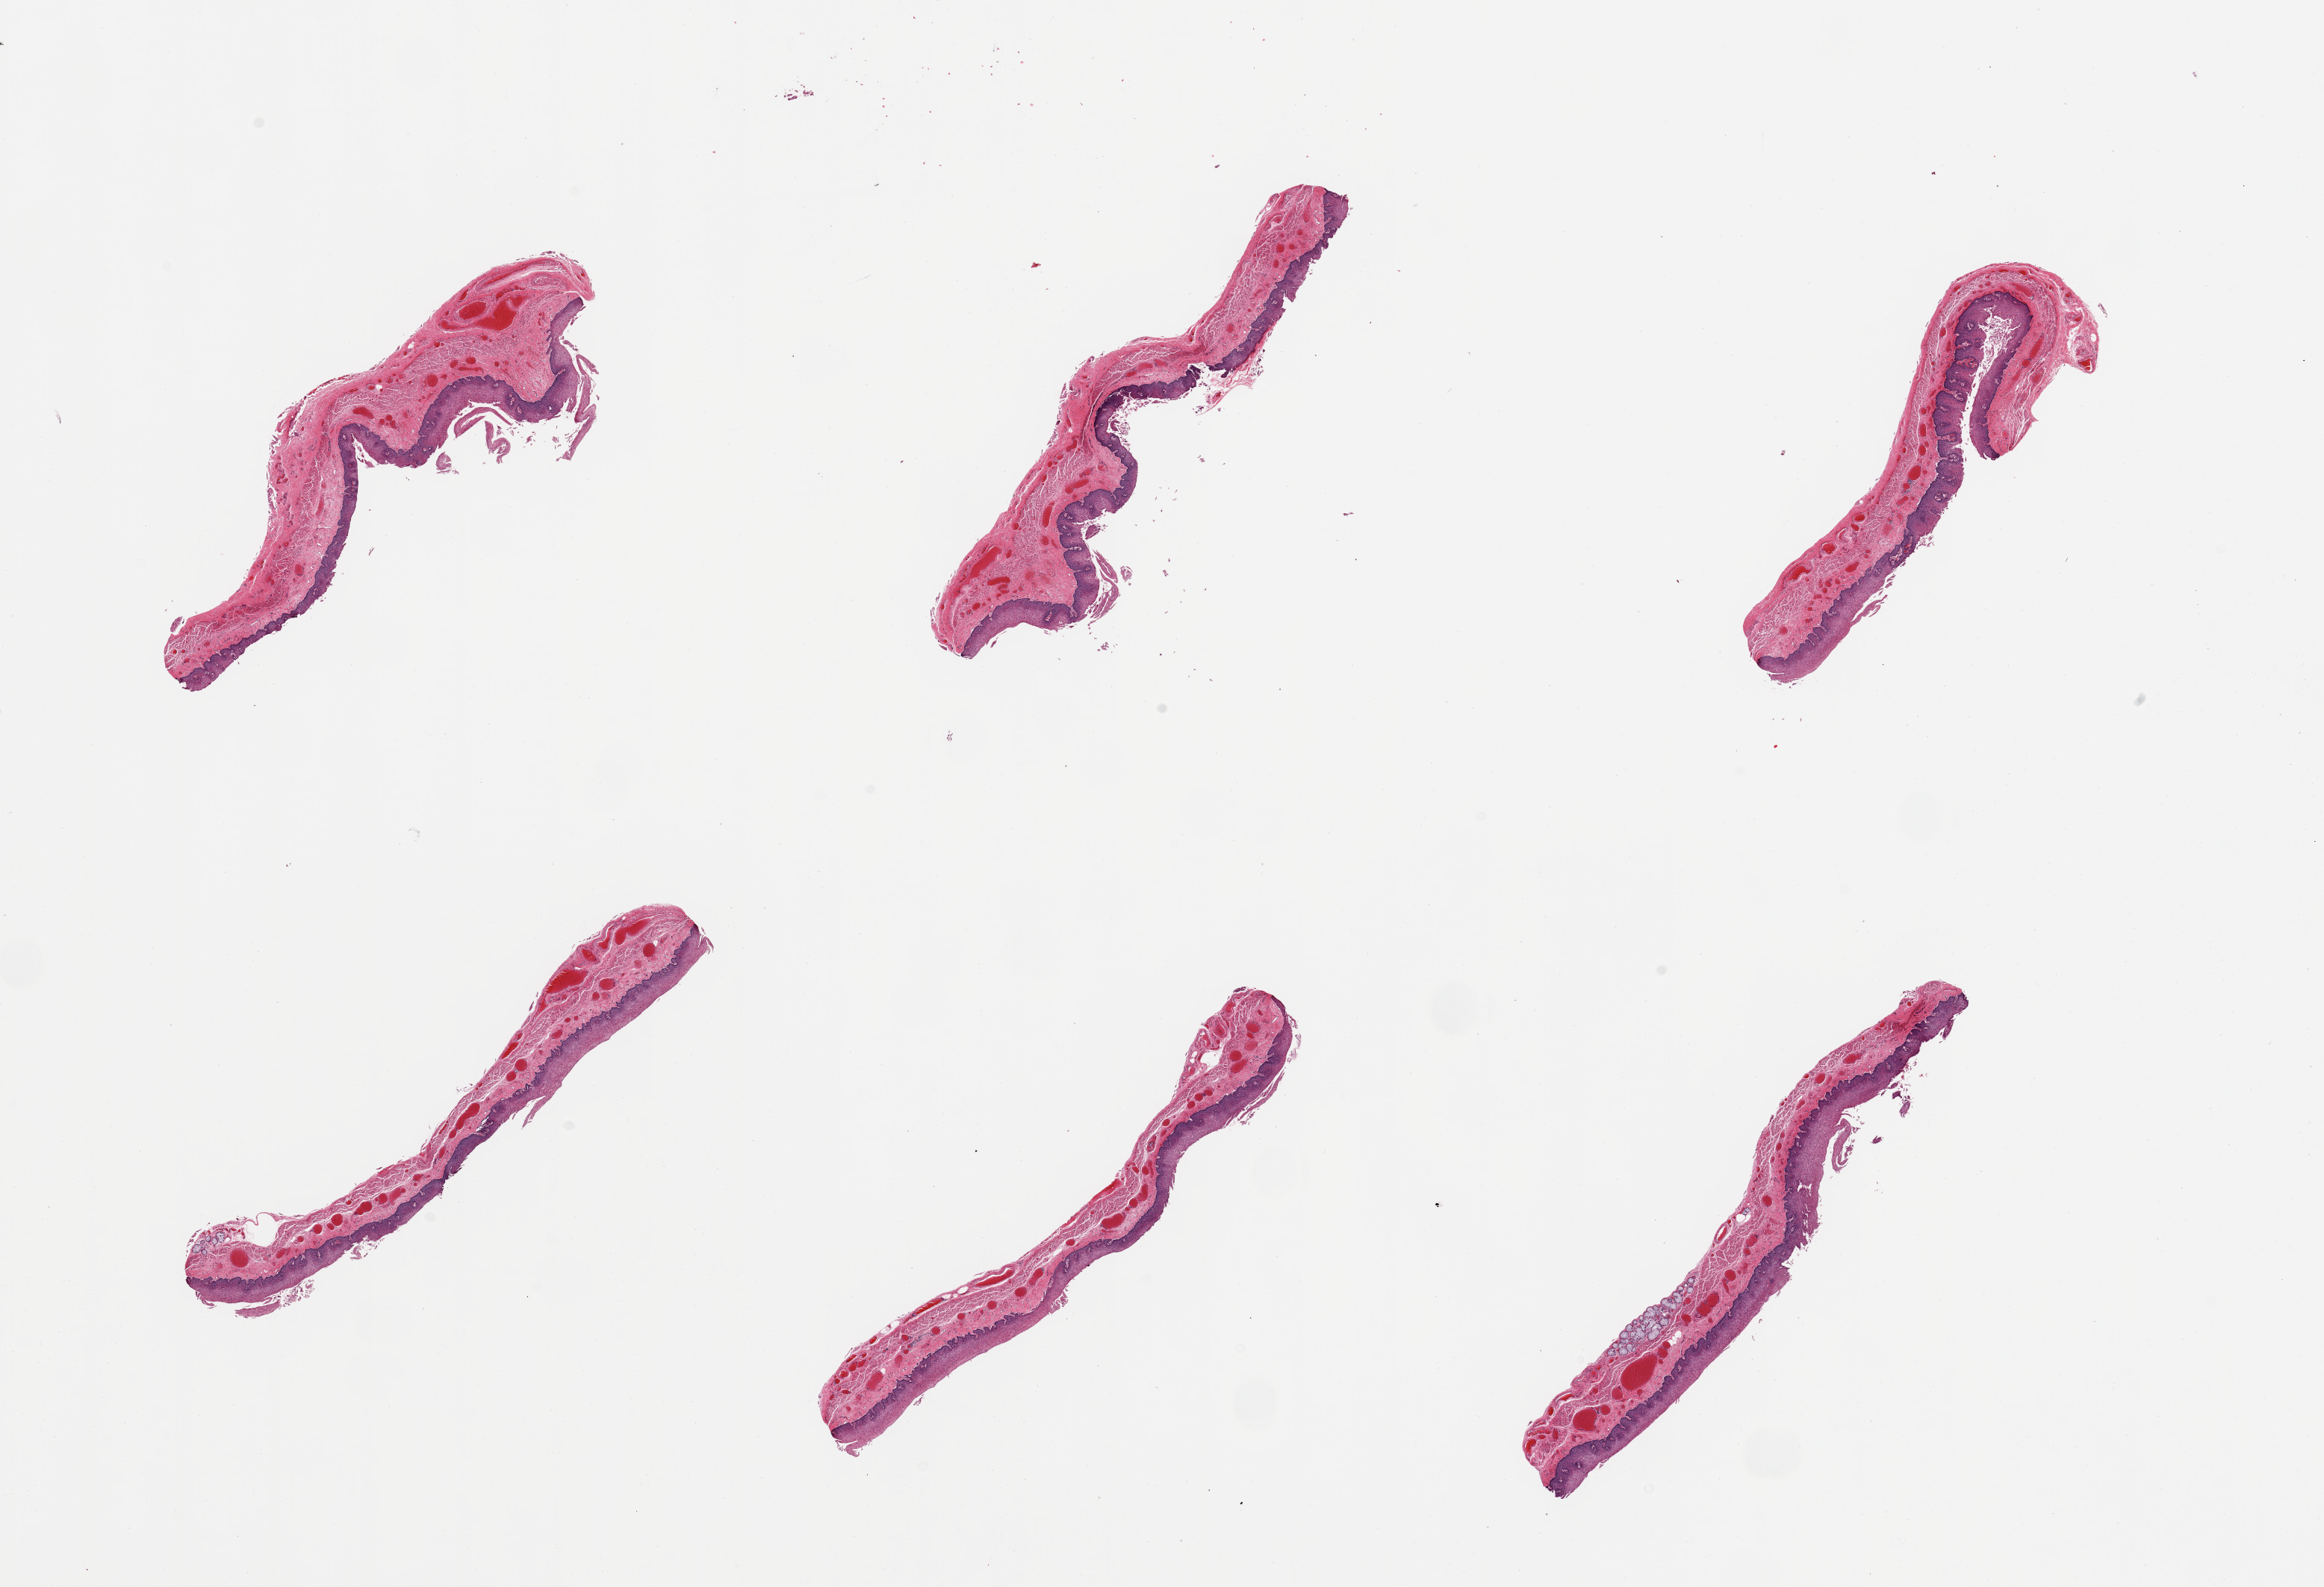
Digitized haematoxylin and eosin-stained section, shown as a low-resolution overview of the whole scanned area (about 24.6 x 16.8 mm), PAXgene-fixed paraffin-embedded (PFPE) section, target tissue: esophageal mucous membrane, donor tissue sample. Donor sex: male.
Reviewer comment on this tissue sample: 6 pieces; congested, few clusters of submucosal glands.